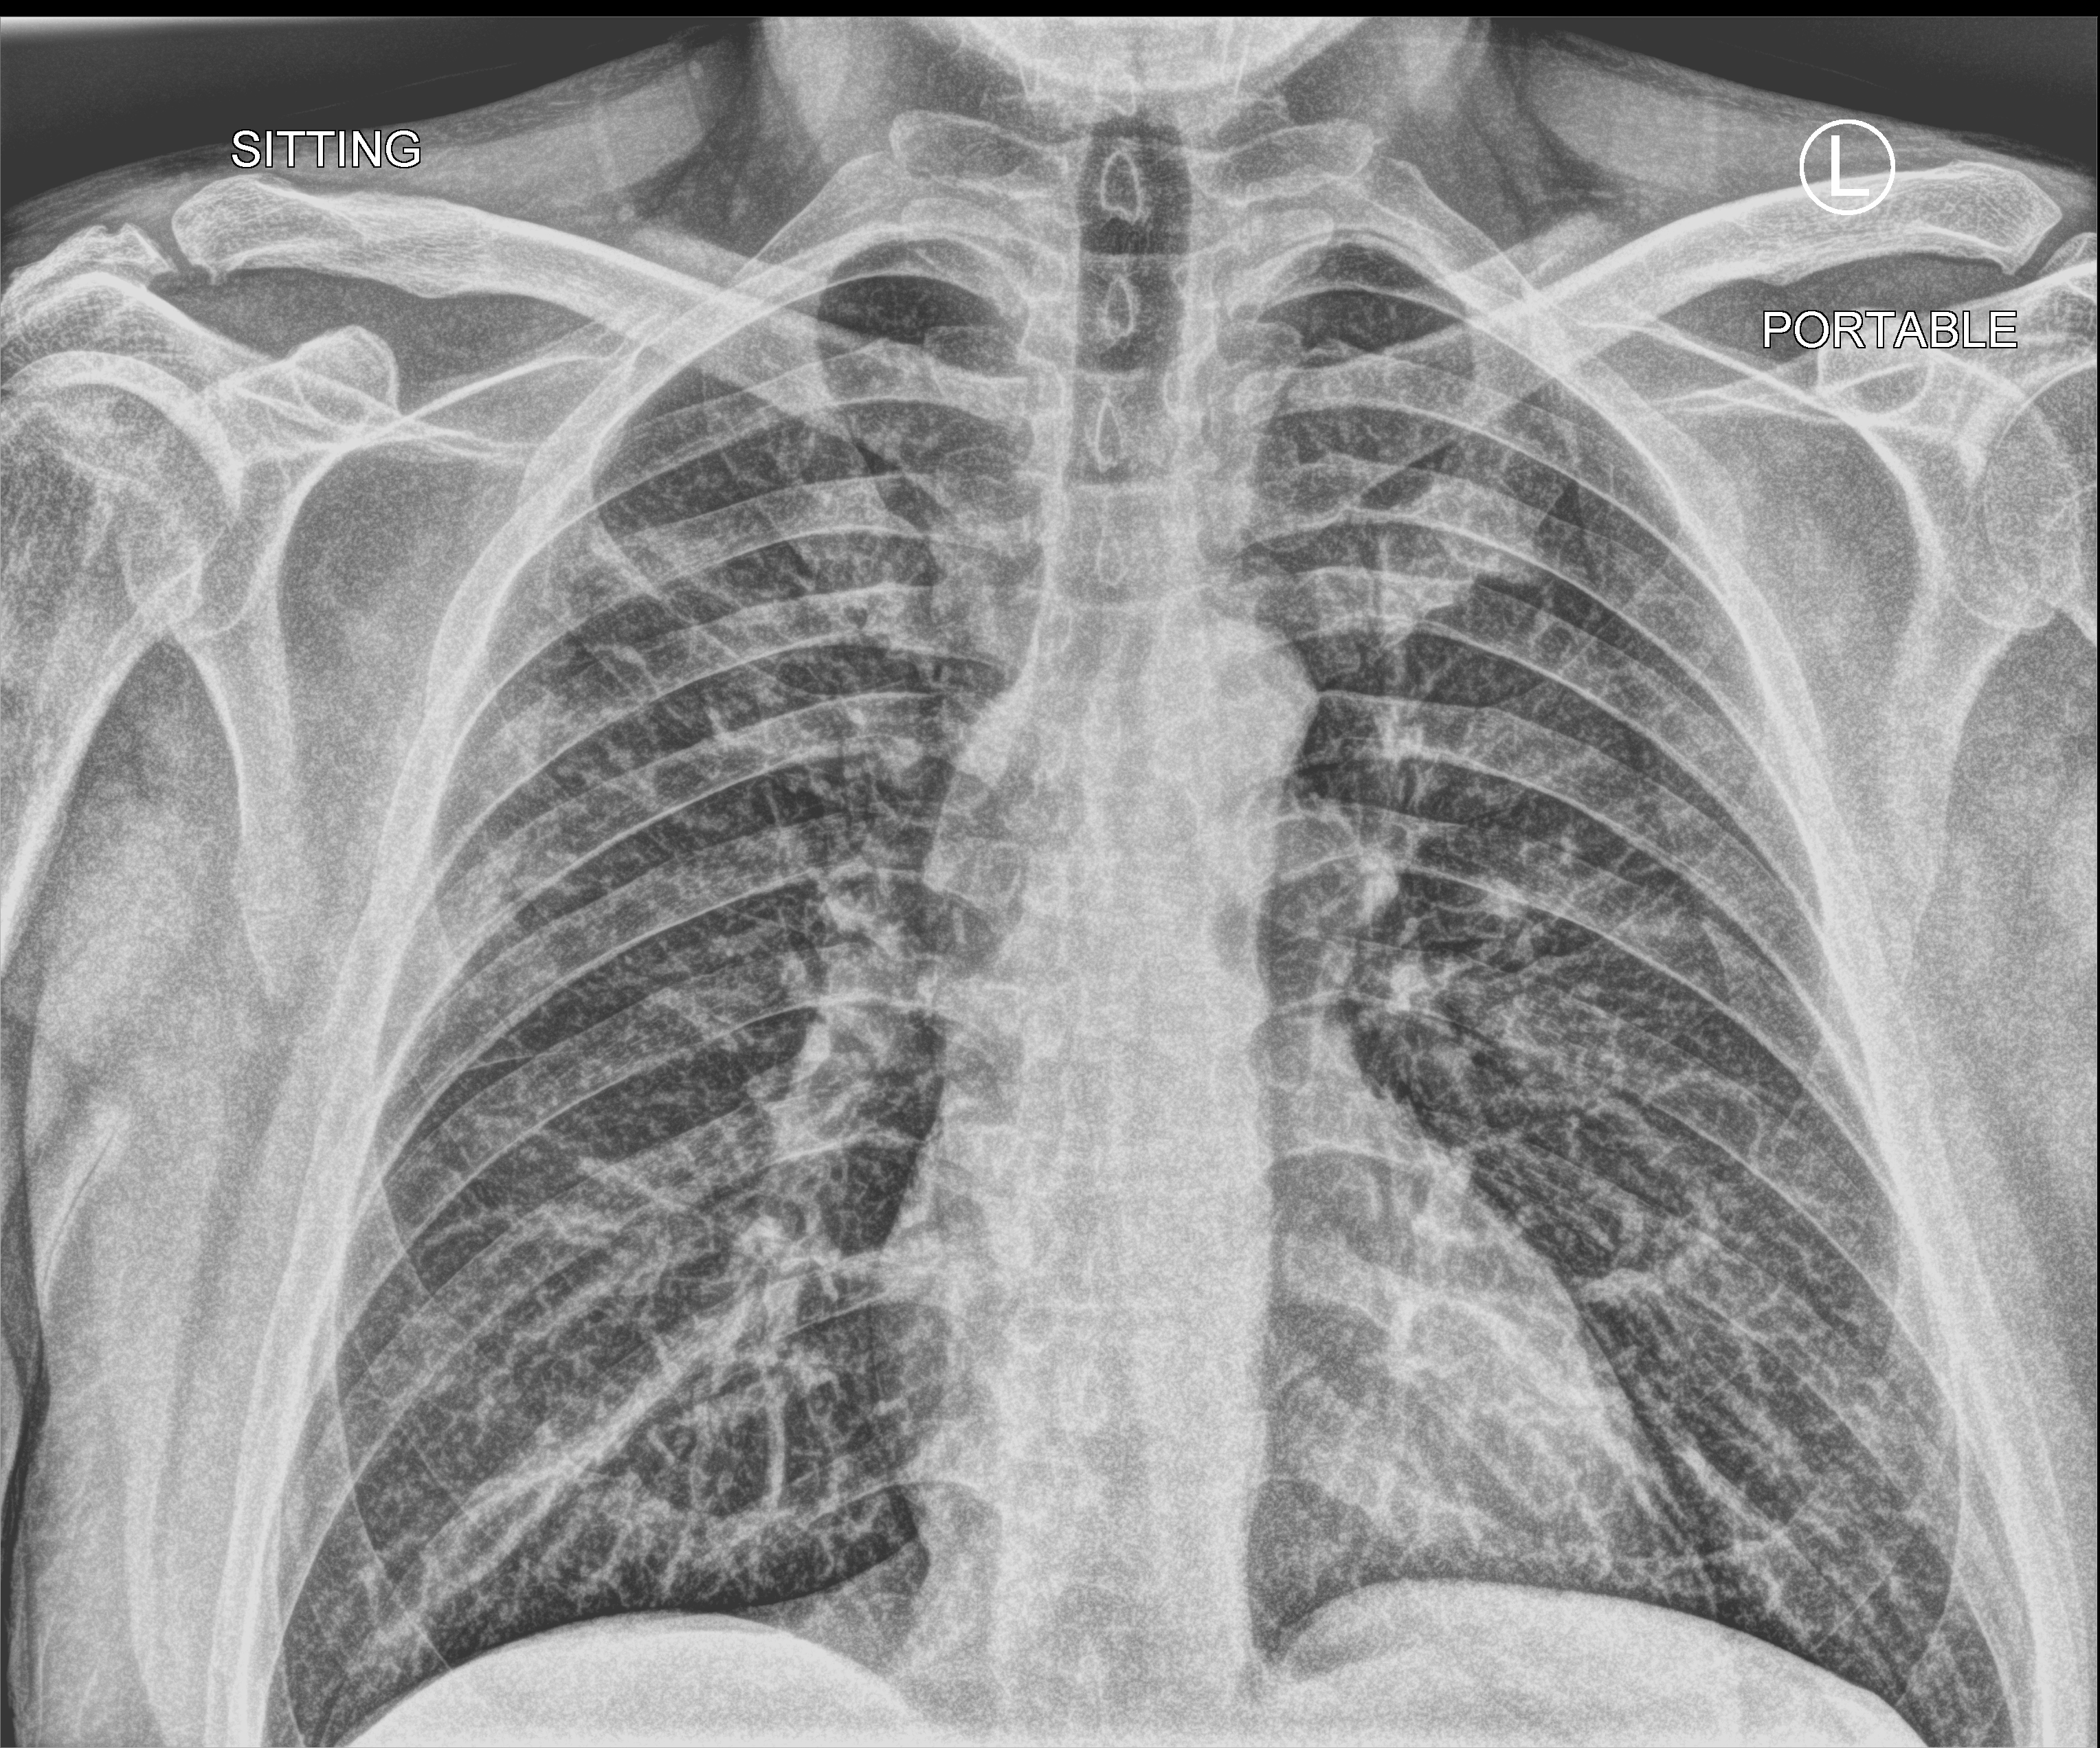
Bedside chest radiograph (computed radiography), anteroposterior (AP) projection. Male patient hospitalised with COVID-19, age 18–59 years.
From the hospital-stay record, not from the radiograph (when in the stay this image was taken is not recorded): length of hospital stay: 1 day; chronic kidney disease (admission record): no.